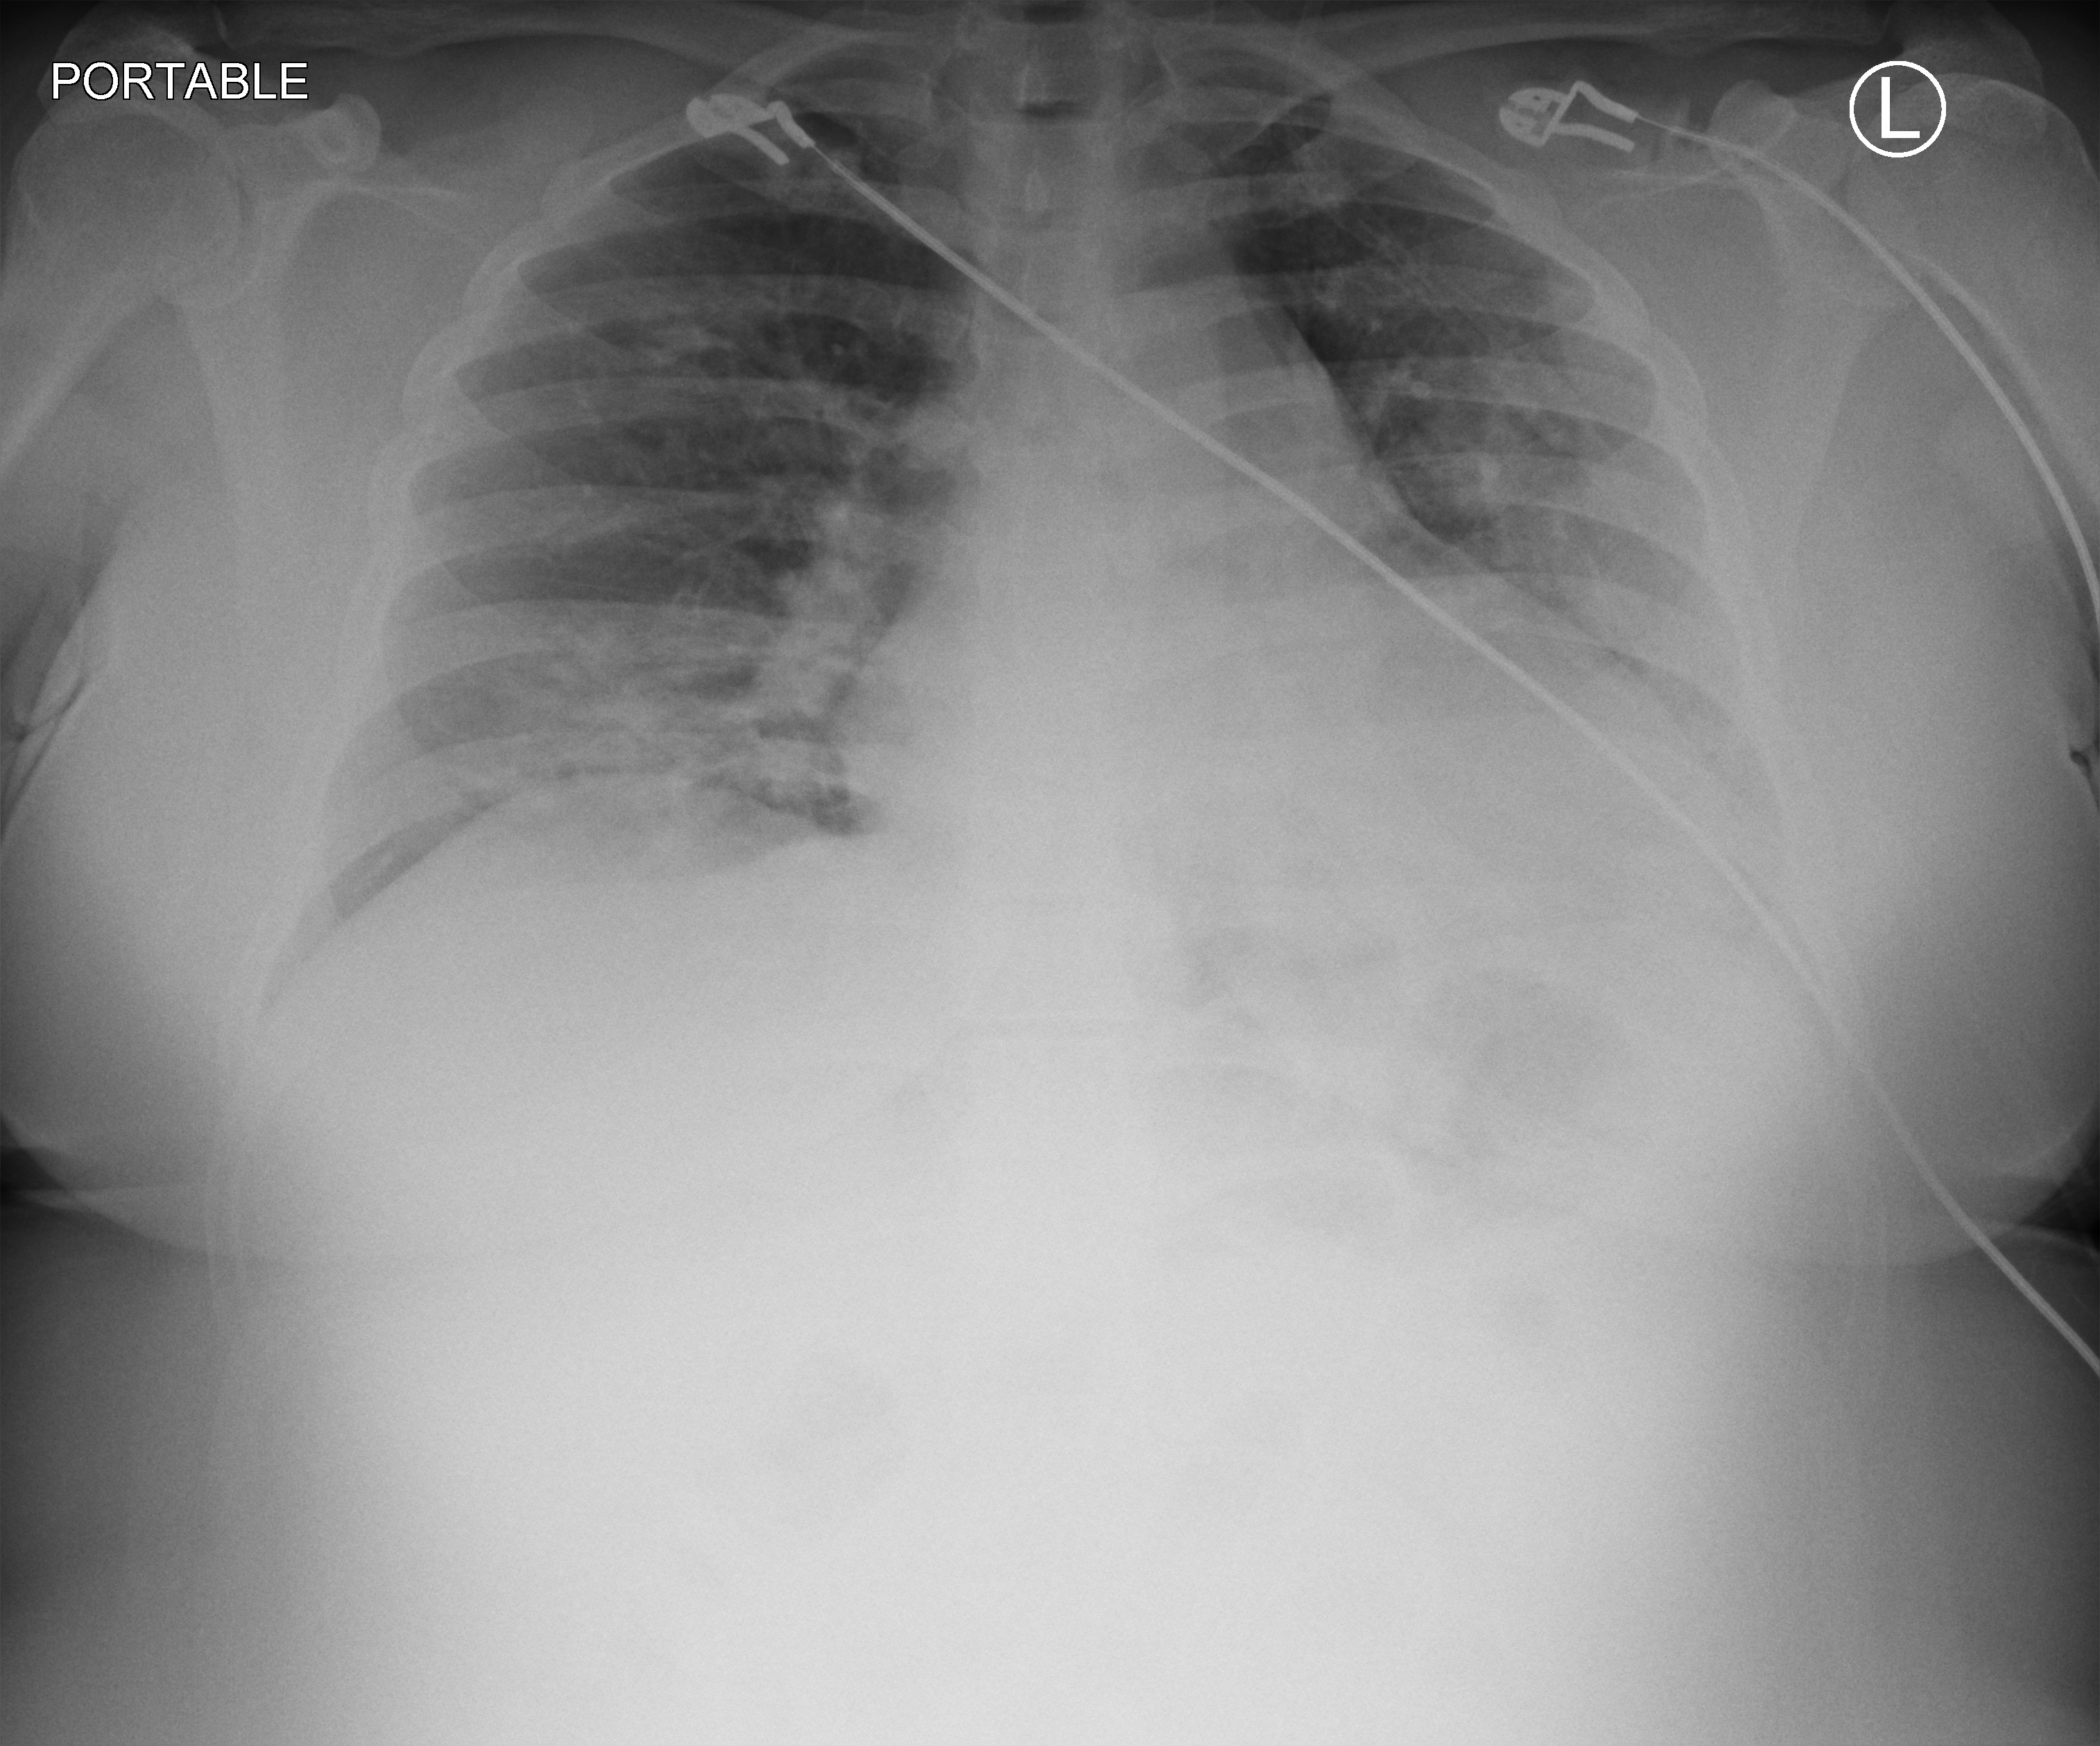
Chest X-ray (portable); anteroposterior (AP) projection. Patient hospitalised with COVID-19; female, aged 18–59 years.
Admission-level facts for this patient (not findings on this image; timing relative to this image not recorded): mechanically ventilated during this hospital stay: no; admitted to intensive care during this hospital stay: no.